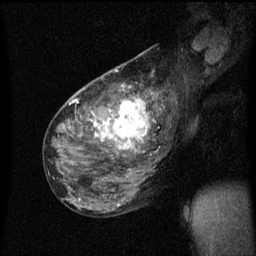
Breast MRI (dynamic contrast-enhanced), one sagittal slice. Position 31 of 60 along the scan axis. Dynamic contrast-enhanced series, image 2 of 3 at this slice position (ordered by acquisition). 1.5 T. TE 4.2 ms, TR 8.4 ms. 2 mm slice thickness. 256 × 256 image matrix. Patient: female, 49 years.
Outlined on this slice (semi-automatic segmentation, software-assisted and operator-edited):
- analysis volume of interest (the breast-tissue region the enhancement analysis was run in; not a lesion): box from (x=103, y=90) to (x=157, y=151) px
- tumour enhancement mask (voxels above the 70 % enhancement threshold inside the analysis volume of interest): (x=103, y=98)–(x=151, y=151)